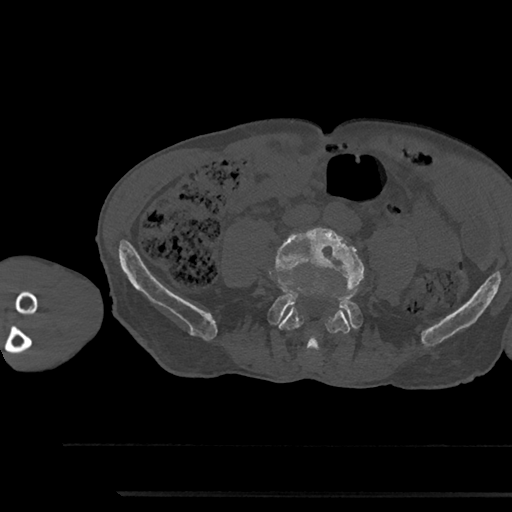
CT including the spine, one axial slice; slice 382 of 797 in the series (ordered by position); 120 kVp; bone window (W 1800 / L 400 HU); 0.5 mm slice thickness; 512 × 512 image matrix, field of view 367 × 367 mm. Male patient, age 79 years. Case-level facts recorded for this patient, not image findings: primary cancer: prostate.
Annotated regions visible in this slice (semi-automatic segmentation, software-assisted and operator-edited):
- L4 vertebra: bounding box (x1, y1, x2, y2) in pixels: (272, 227, 364, 352)
- L5 vertebra: (270, 294, 362, 329)